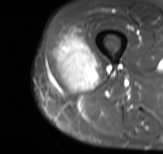
MRI of an extremity soft-tissue mass, one axial slice; slice 28 of 61 in the series (ordered by position); STIR; MR volume resampled by the dataset authors to the PET/CT grid (not the native acquisition matrix); 163 × 154 image matrix, field of view 159 × 150 mm. Male patient. Case-level facts recorded for this patient, not image findings: histological type: poorly differentiated synovial sarcoma; grade: high; site of the primary tumour: right buttock.
Outlined on this slice (expert contour drawn on MRI and transferred to this co-registered scan by the dataset authors):
- gross tumour volume including surrounding oedema: bounding box (x1, y1, x2, y2) in pixels: (55, 25, 99, 92)
- gross tumour volume (mass): (57, 36, 99, 92)